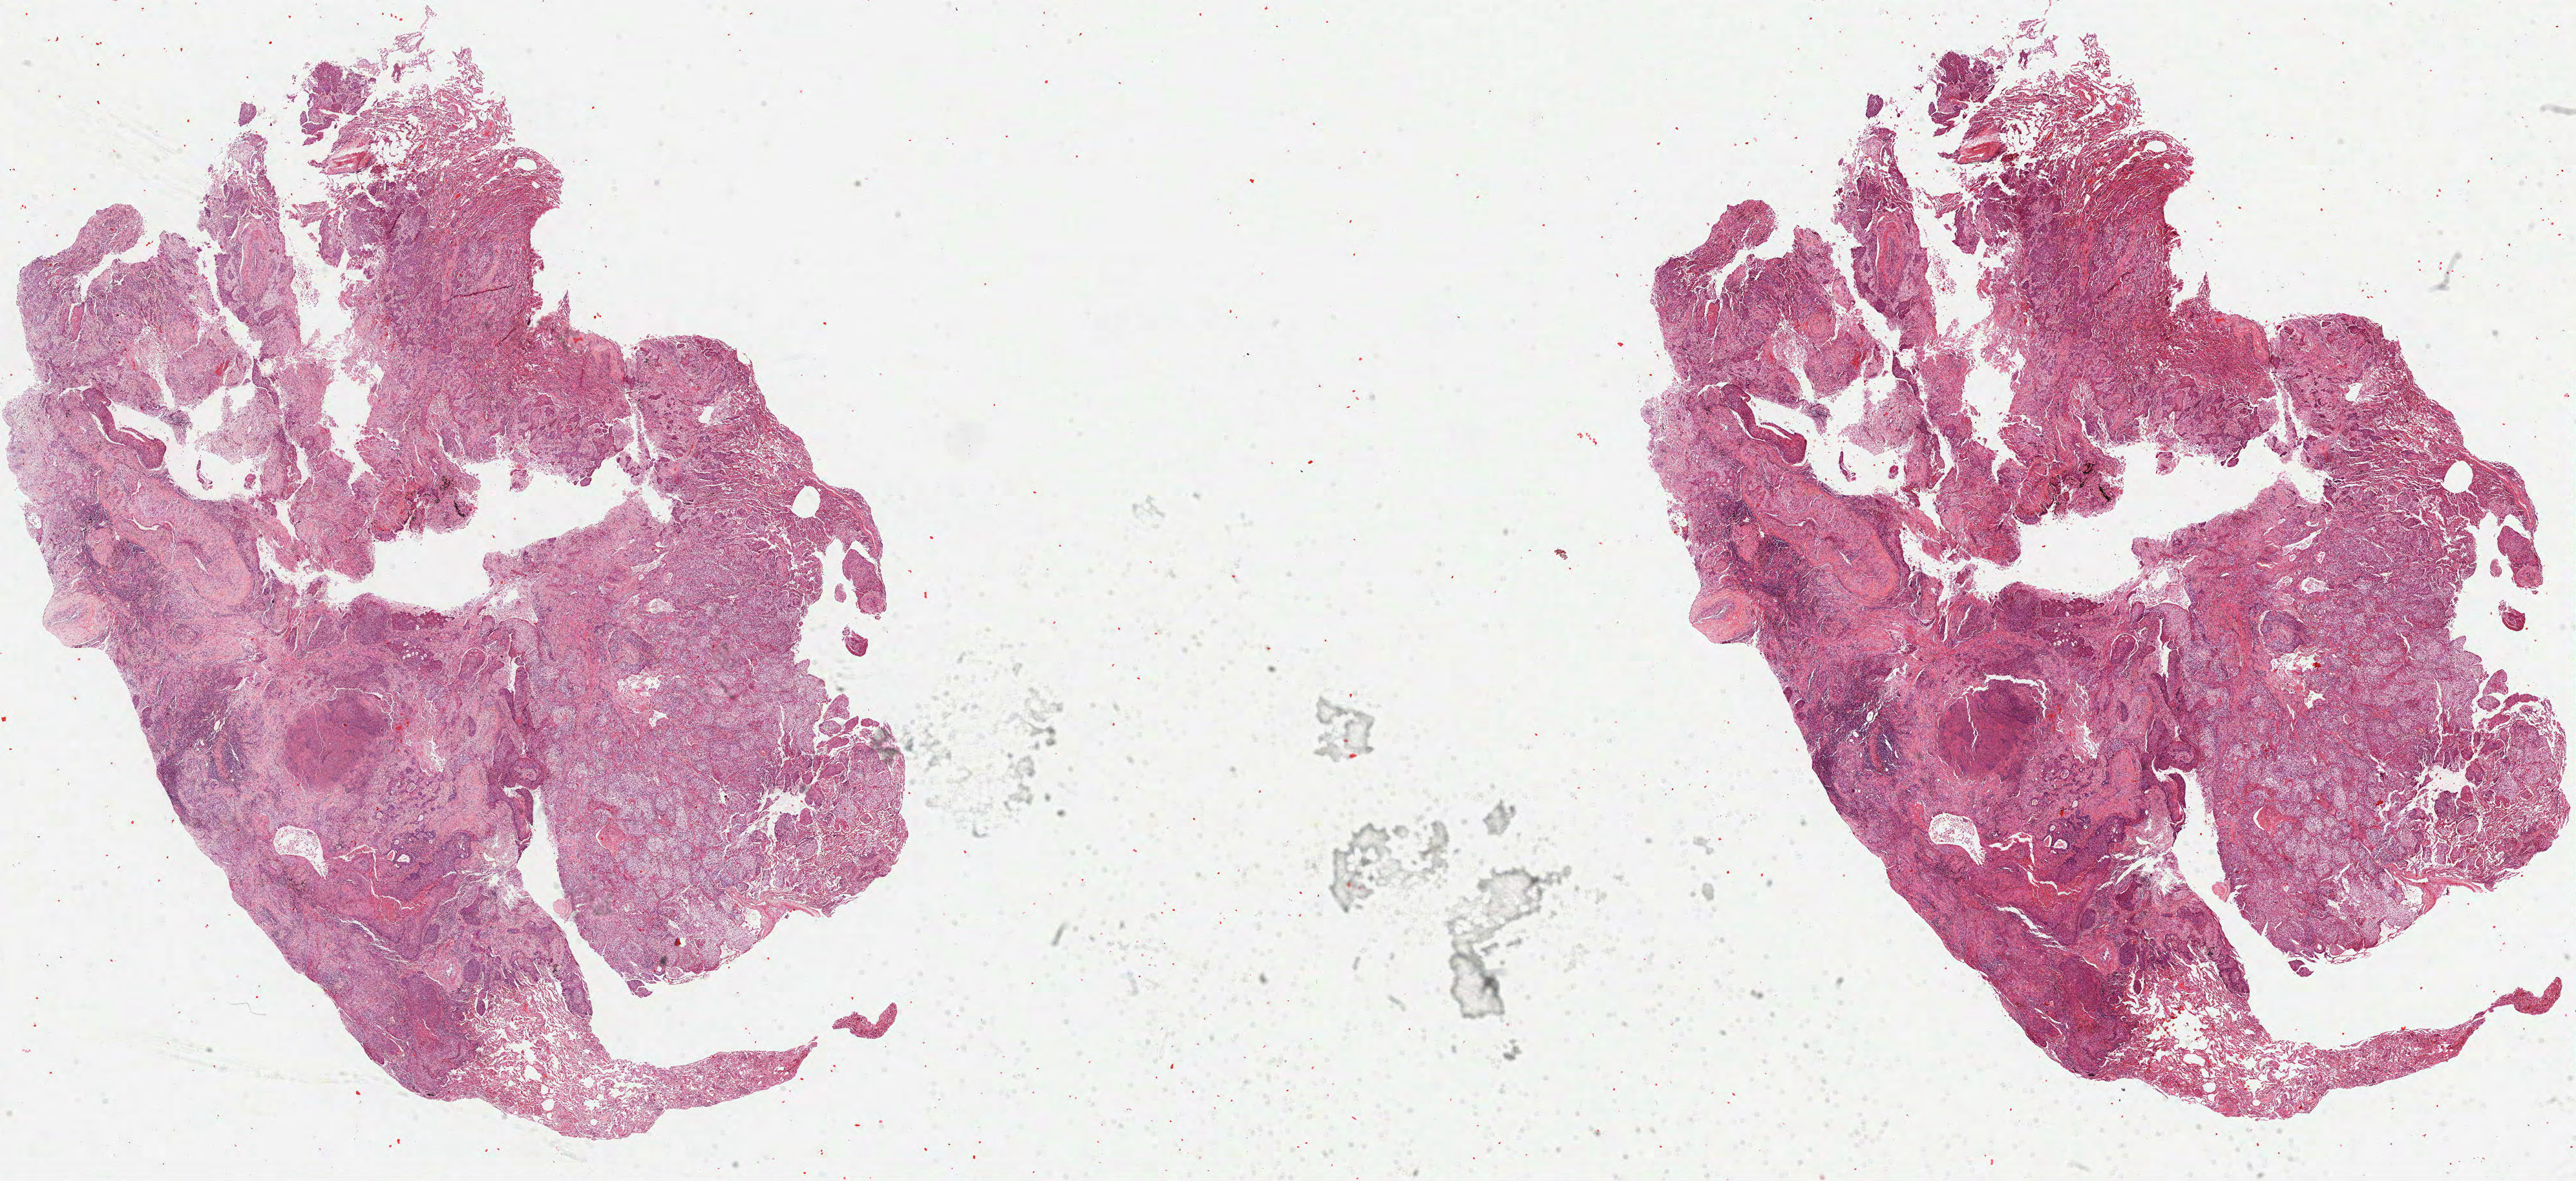
Digitized H&E-stained tissue section (whole slide) — low-resolution overview of the scanned area, about 32.1 x 14.7 mm (slide scanned at 40x), formalin-fixed paraffin-embedded (FFPE) diagnostic section, primary tumour sample from the lung. Male, age 76 years at initial diagnosis.
- histologic diagnosis: Squamous cell carcinoma, NOS
- AJCC pathologic stage: IA
- TNM: T1a N0 M0